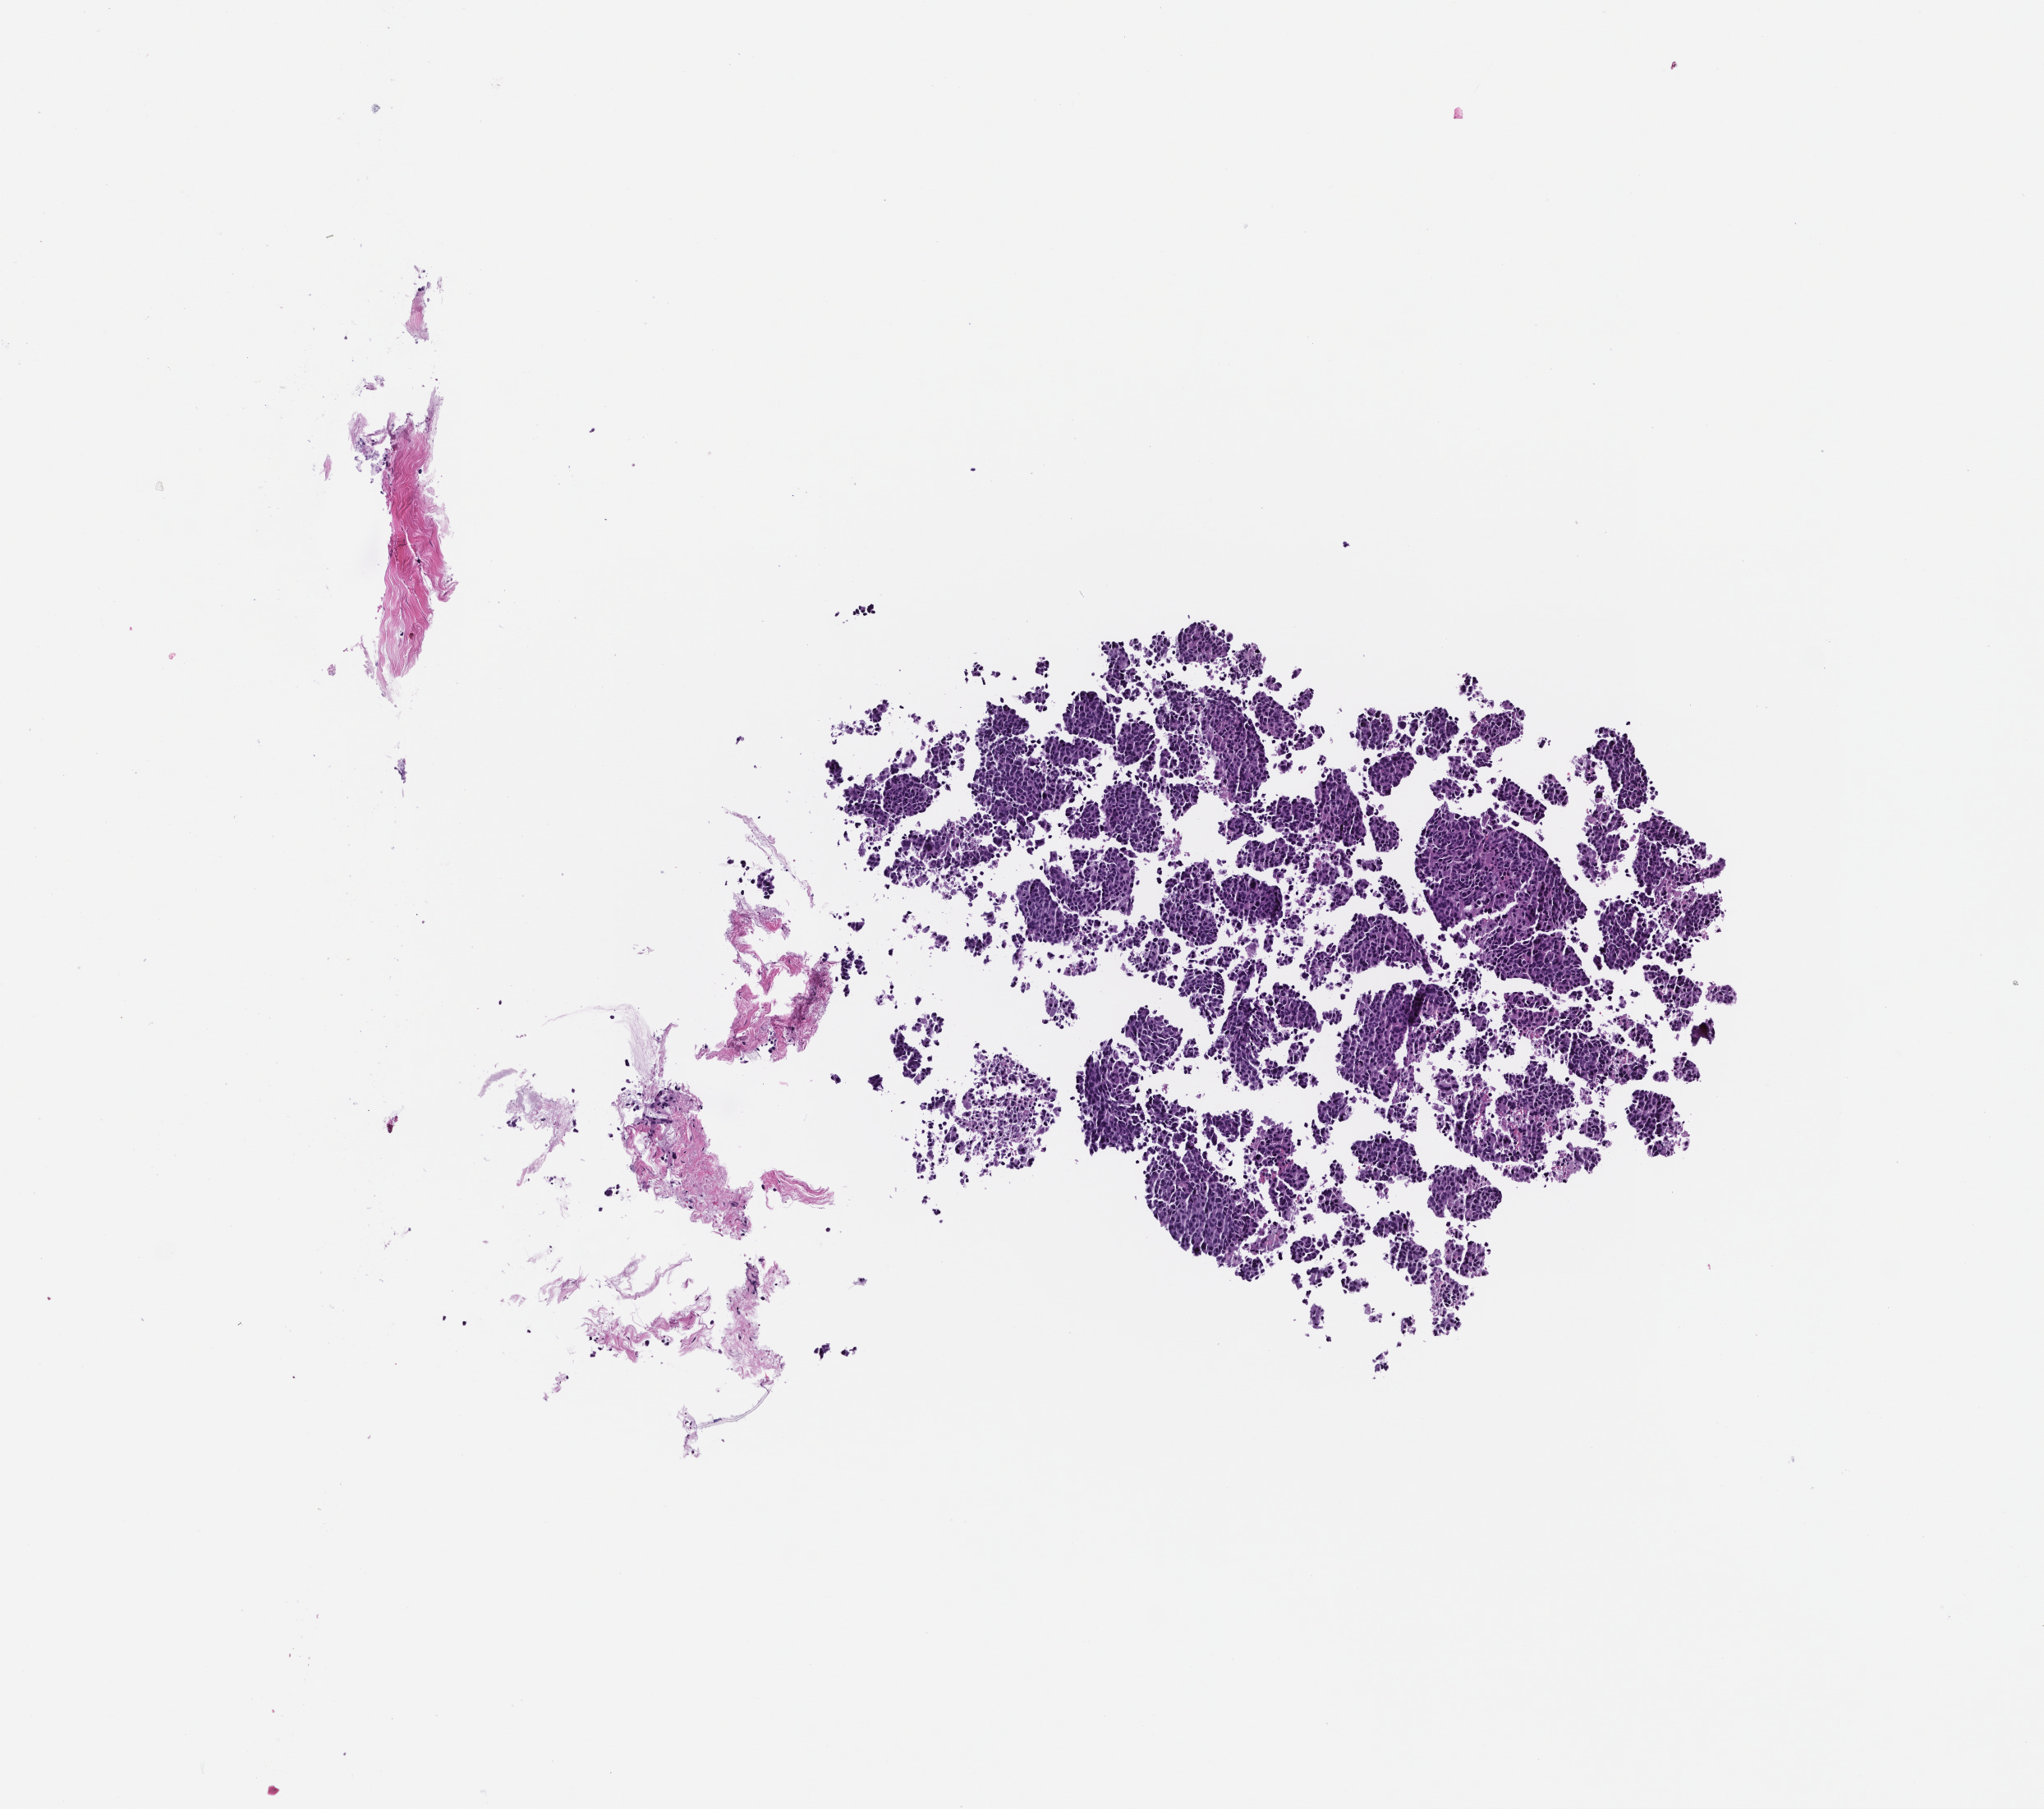
H&E whole-slide image, whole scanned area (about 5.0 x 4.4 mm) shown as a low-resolution overview, FFPE section, specimen time point: archival tissue. Patient sex: female.
• this section: metastatic tumor tissue
• primary diagnosis of the patient: Non-Small Cell Lung Carcinoma